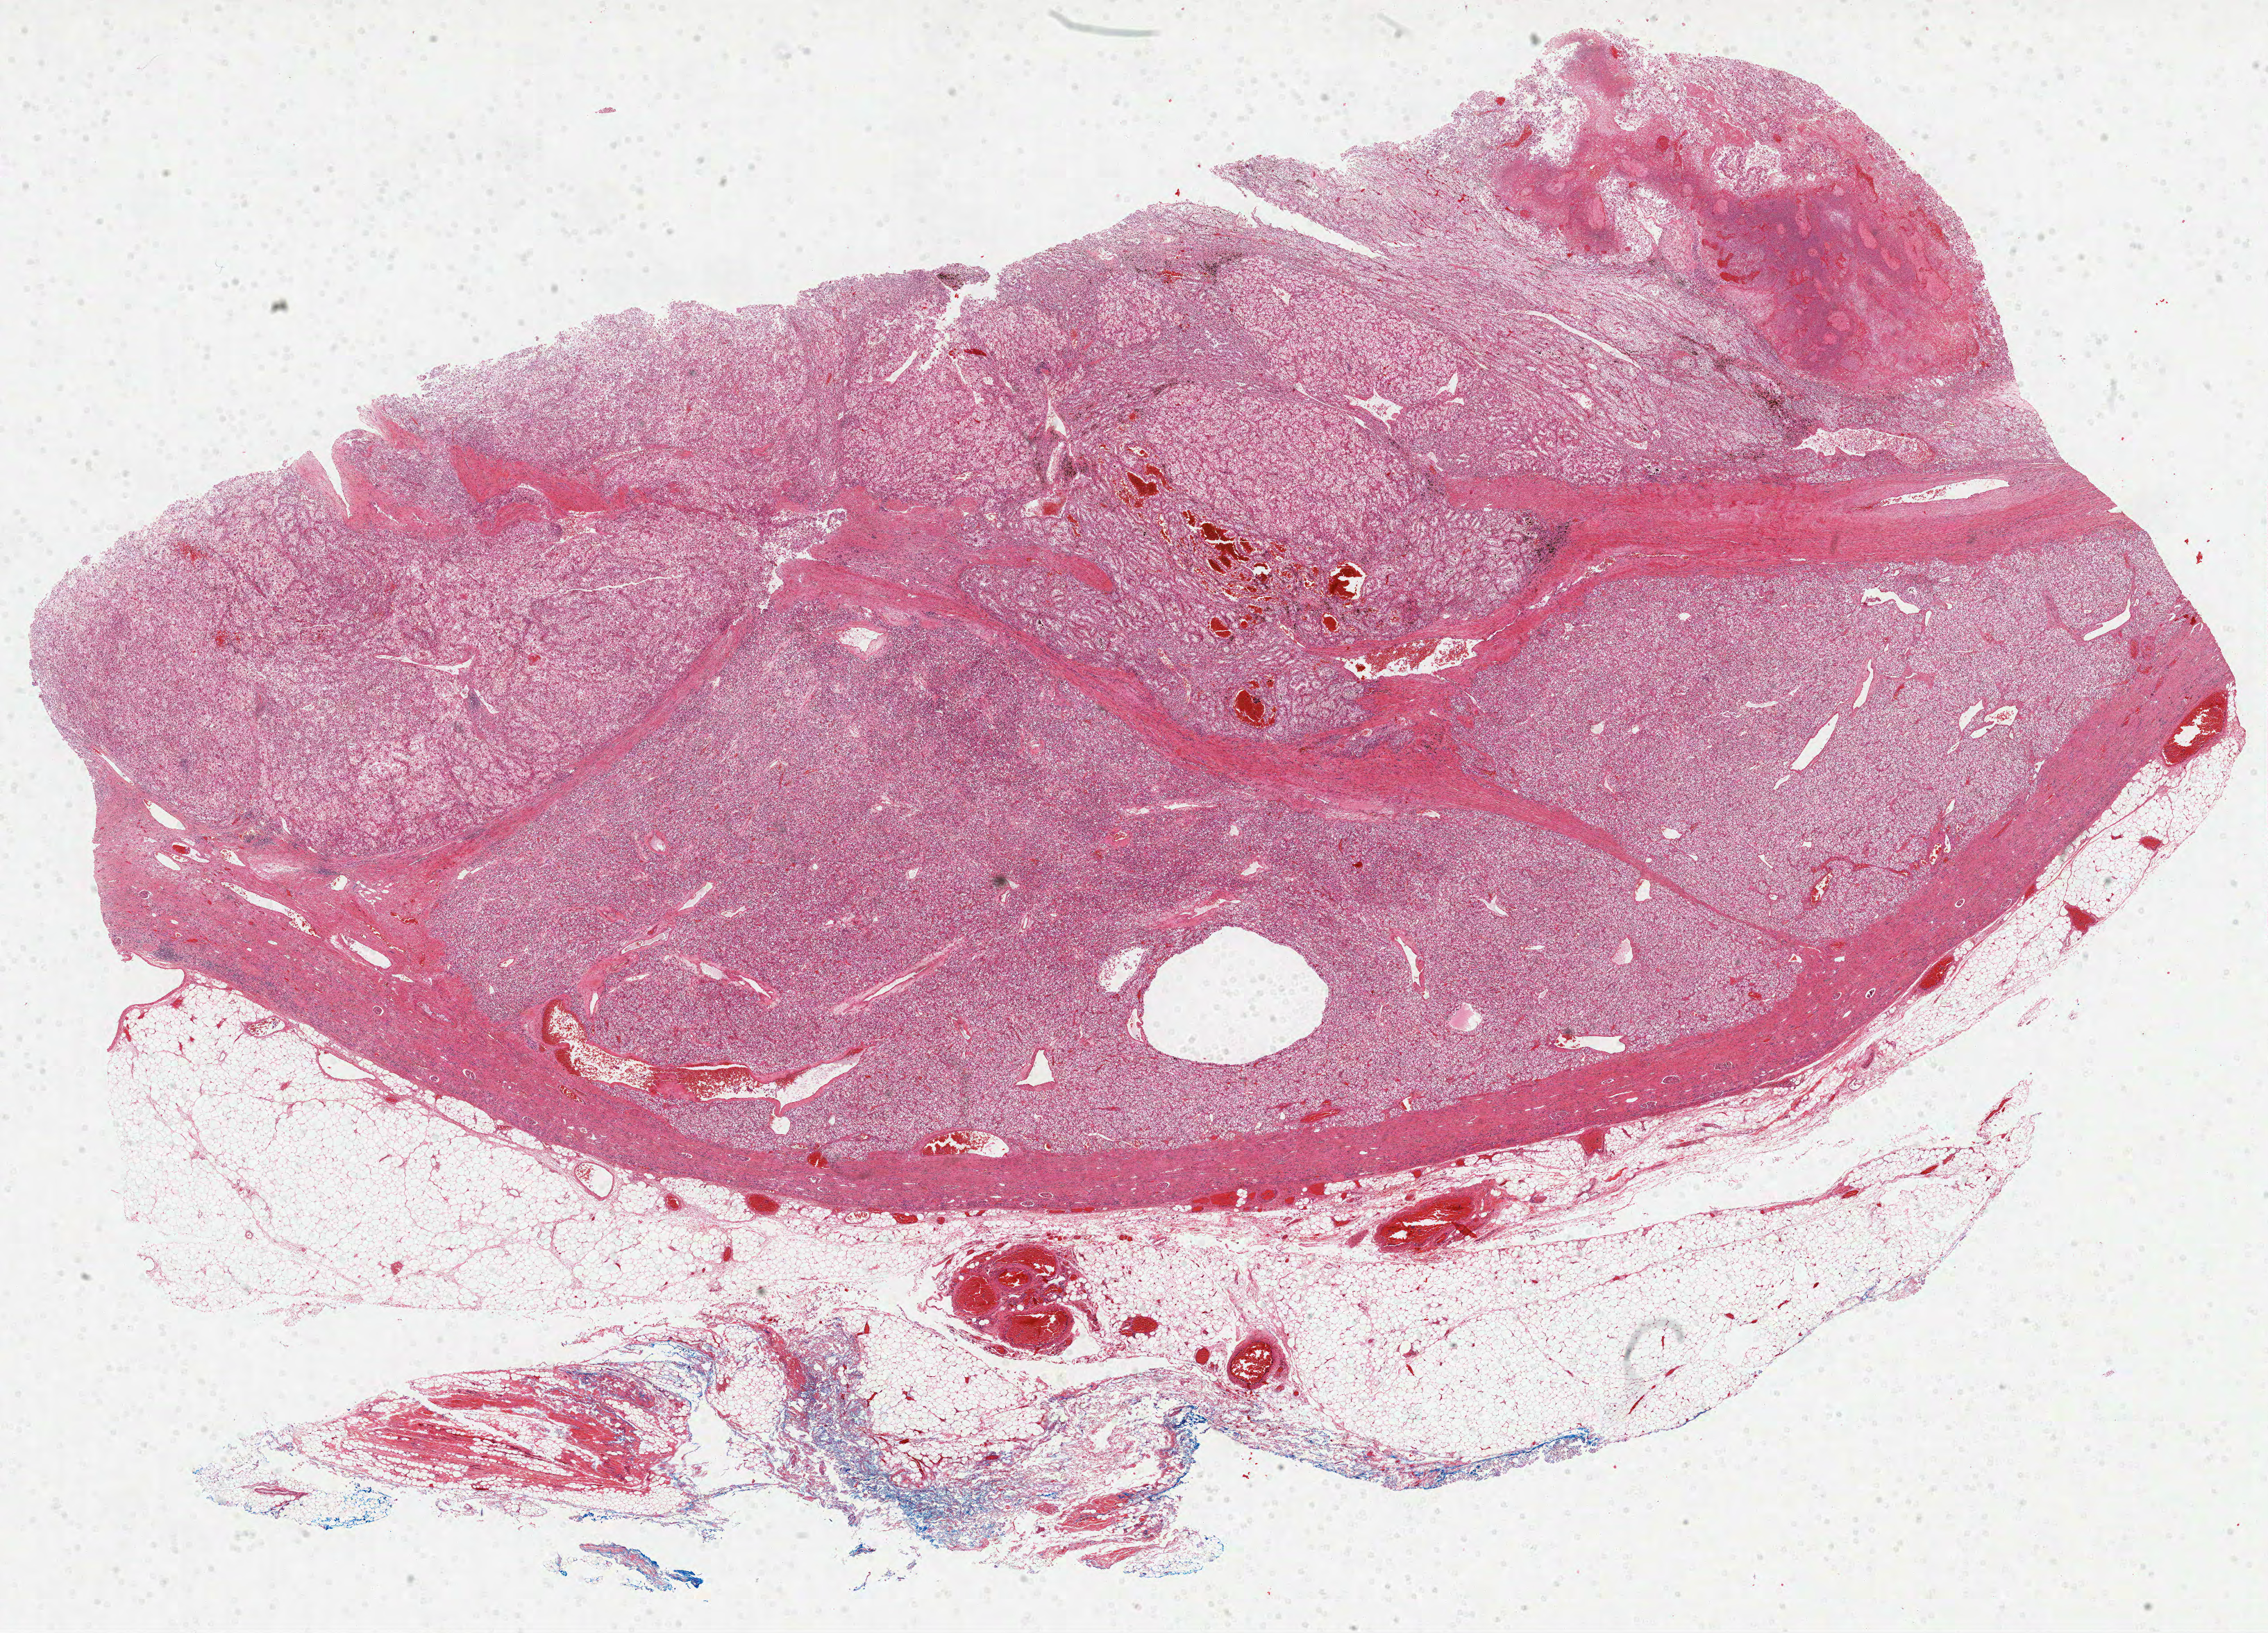
Hematoxylin and eosin (H&E) stained whole-slide image, whole scanned area (about 26.3 x 19.0 mm, slide scanned at 40x) shown as a low-resolution overview; formalin-fixed paraffin-embedded (FFPE) diagnostic section; sample: primary tumour, kidney. Female patient; age at initial diagnosis 59 years. Histologic grade: G4 (undifferentiated).
* histologic diagnosis: Clear cell adenocarcinoma, NOS
* TNM: T3b N0 M0
* AJCC pathologic stage: III (6th edition)